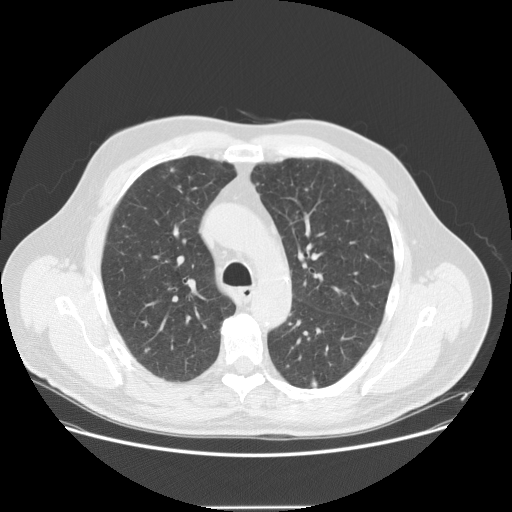
Low-dose screening chest CT, one axial slice. Slice 101 of 143 in the series (ordered by position). Reconstruction kernel STANDARD. Lung window (W 1500 / L -600 HU). 2.5 mm slice thickness. 512 × 512 image matrix, field of view 400 × 400 mm.
Outlined on this slice (expert manual segmentation):
- lesion 2 (tumor): box from (x=311, y=379) to (x=318, y=388) px